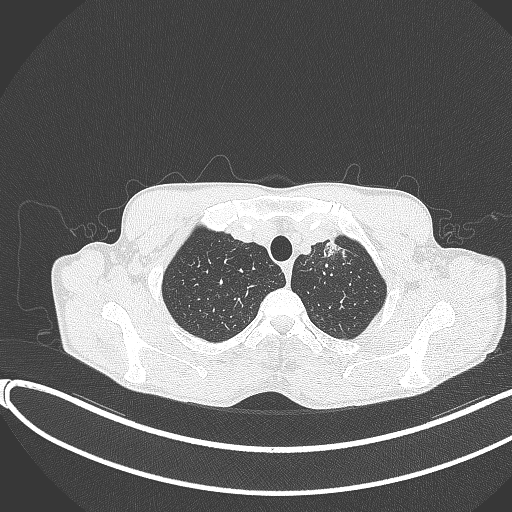
Chest CT, one axial slice. Reconstruction kernel B70f. Lung window (W 1500 / L -600 HU). 512 × 512 image matrix, field of view 400 × 400 mm. Patient: male, 58 years. From the clinical record (not read from this slice): clinical TNM (as recorded): T1c N1 M0.
Structures marked on this image (rectangle marked by the reading radiologist):
- lung tumour (recorded histology: adenocarcinoma): bounding box (x1, y1, x2, y2) in pixels: (316, 230, 341, 264)